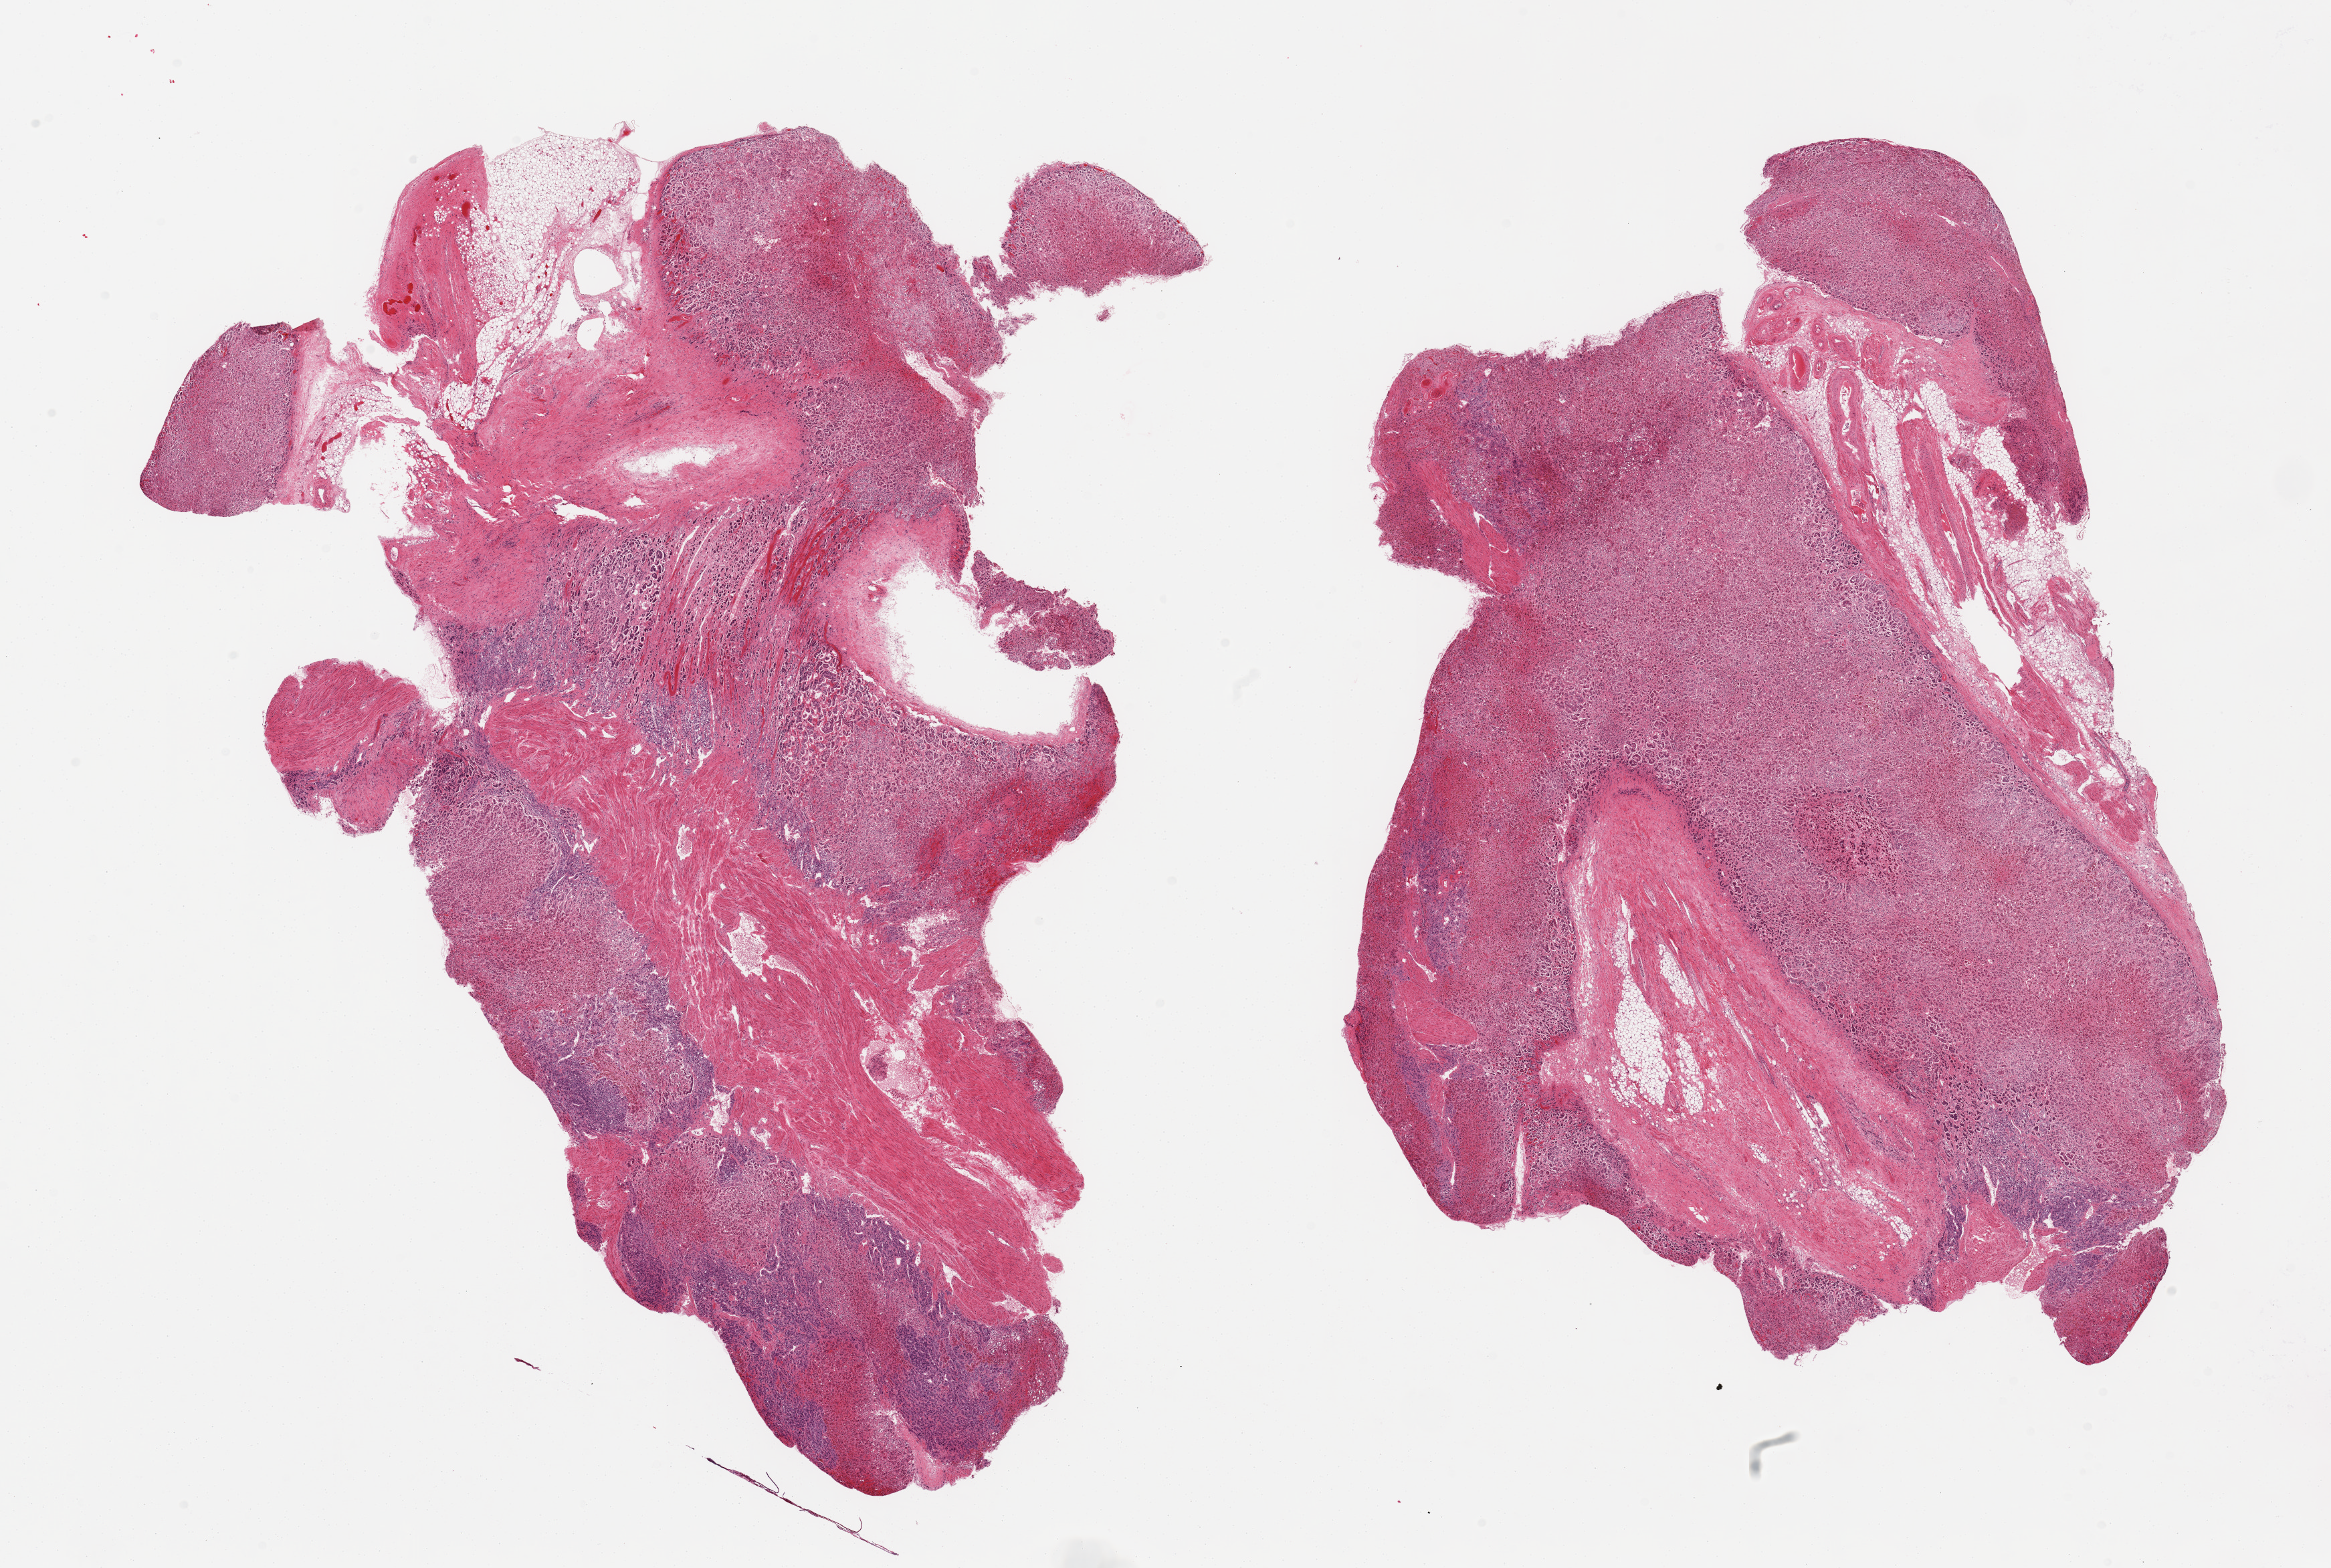
Digitized hematoxylin and eosin (H&E)-stained section, shown as a low-resolution overview of the whole scanned area (about 27.6 x 18.5 mm), PAXgene-fixed paraffin-embedded (PFPE) section, sampled site (target tissue): adrenal gland, donor tissue sample. Donor: male.
Reviewer comment on this tissue sample: 2 pieces; oversized, cortex and medulla, ~30% is fat/fibrous.